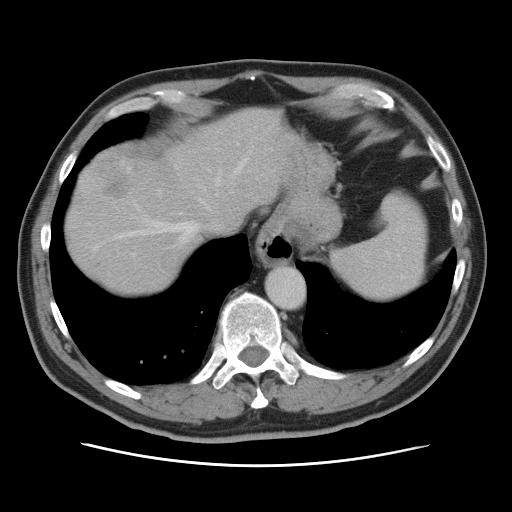
Contrast-enhanced abdominal CT, one axial slice; position 66 of 80 along the scan axis; 120 kVp; intravenous contrast given; soft-tissue window (W 400 / L 40 HU); 5 mm slice thickness; 512 × 512 image matrix, field of view 370 × 370 mm. Male patient, age 69 years. From the clinical record (not read from this slice): diagnosis: colorectal cancer liver metastases, imaged before liver resection; multiple liver metastases: no; largest metastasis: 5 cm; disease in both lobes: yes.
Annotated regions visible in this slice (expert manual segmentation):
- hepatic veins: box from (x=94, y=152) to (x=252, y=251) px
- liver: (x=66, y=108)–(x=280, y=294)
- planned liver remnant (the part of the liver to remain after resection): (x=66, y=109)–(x=281, y=295)
- portal vein (with intrahepatic branches): (x=132, y=253)–(x=135, y=256)
- liver metastasis: (x=94, y=155)–(x=142, y=199)